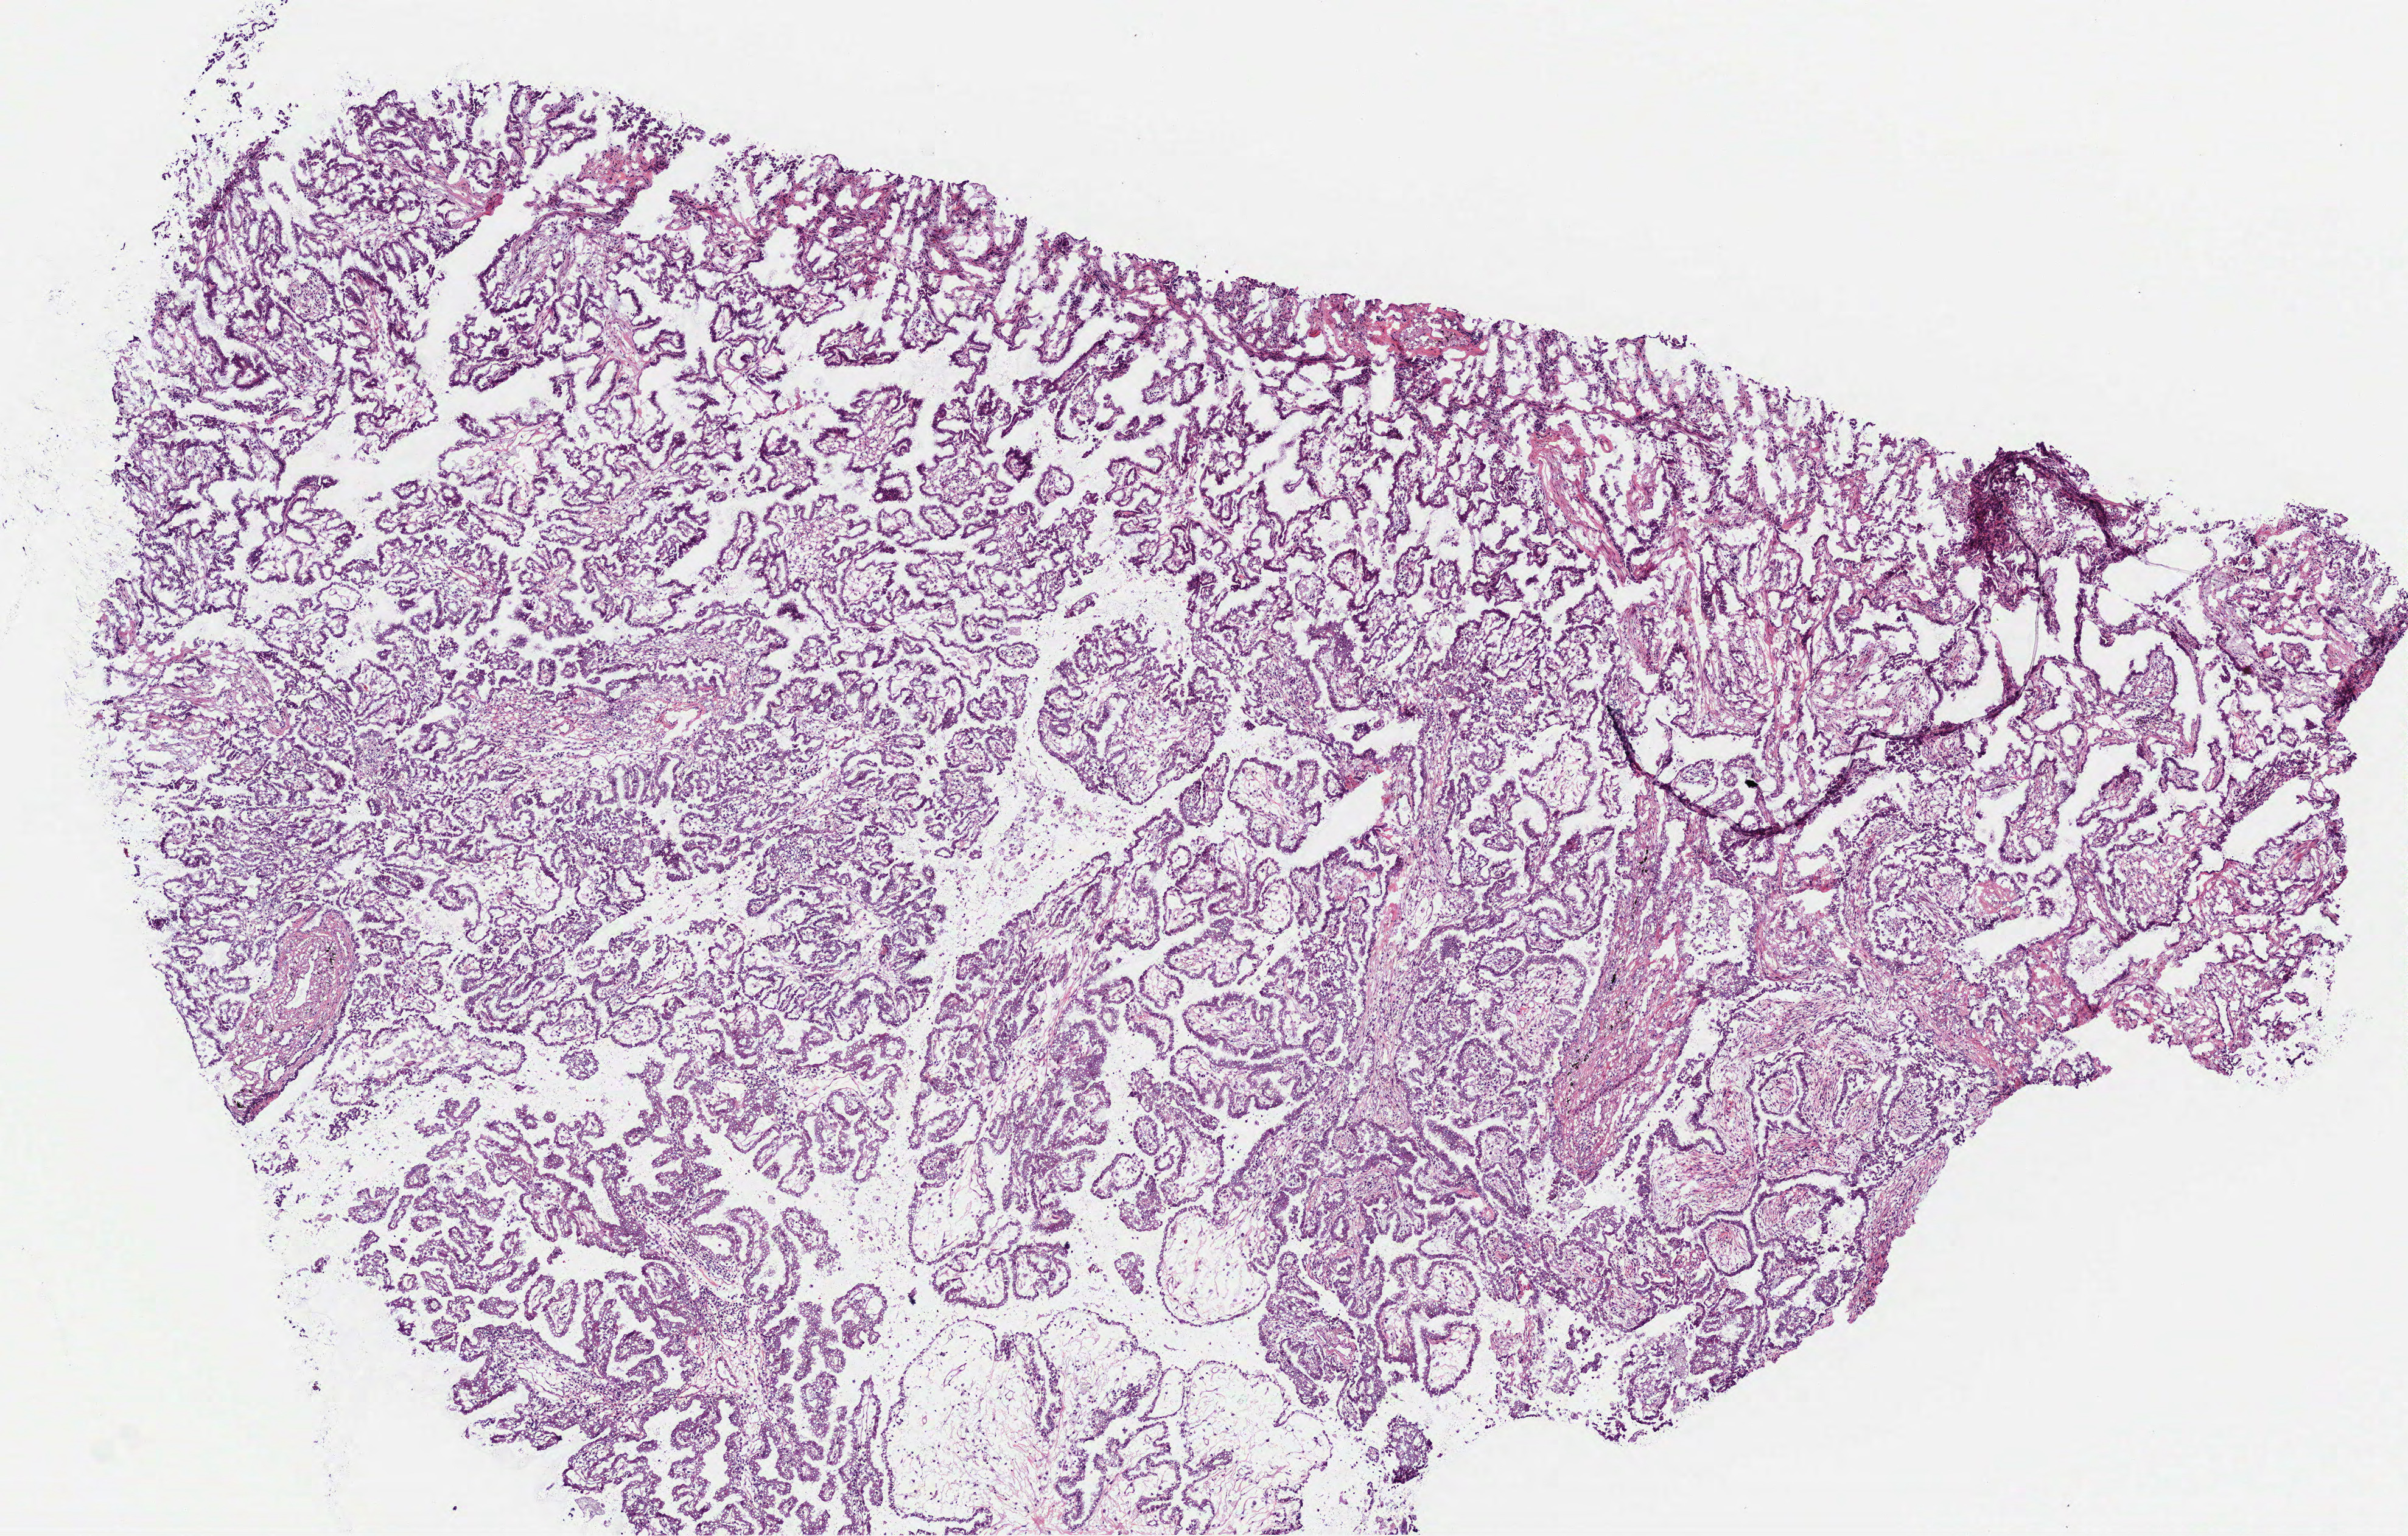
Digitized H&E-stained tissue section (whole slide) — low-resolution overview of the scanned area, about 8.0 x 5.1 mm; frozen section from the bottom of the tissue portion; sample: primary tumour, lung. Patient: male, age at initial diagnosis 72 years. Slide review estimates, as recorded: tumour cells 100%, tumour nuclei 80%, normal cells 0%, stromal cells 0%, necrosis 0%. Inflammatory infiltration, as recorded: lymphocyte infiltration 10%, monocyte infiltration 0%, neutrophil infiltration 0%.
AJCC pathologic stage: IB (6th edition). Diagnosis: Adenocarcinoma with mixed subtypes (upper lobe, lung).